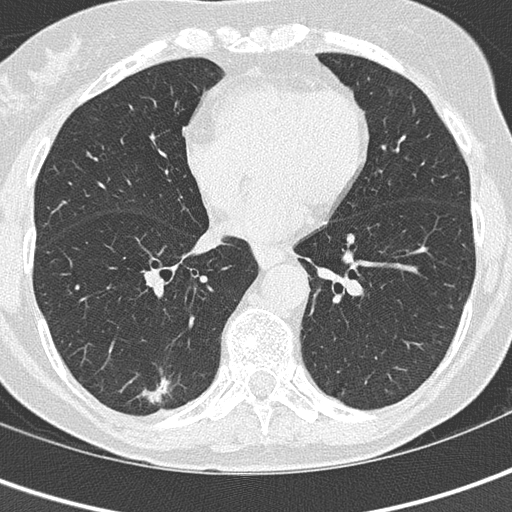
Axial slice from a low-dose chest CT screening exam, second screening round (one year after baseline), lung window (W 1500 / L -600 HU), 2 mm slice thickness, 120 kVp, slice 92 of 152 in the series. Female participant, aged 69 years at enrolment. Current smoker at enrolment.
Lesion marked by an expert reader, bounding box [x1, y1, x2, y2] px = [123, 363, 184, 422]. The screening reader recorded 2 non-calcified nodules or masses ≥4 mm on this exam; which of them this box marks is not recorded. Official screen result: positive, other. Lung cancer was diagnosed 112 days after this screen: adenocarcinoma, NOS, right lower lobe, moderately differentiated (G2), stage IA (AJCC 6th edition), 16 mm at pathology.